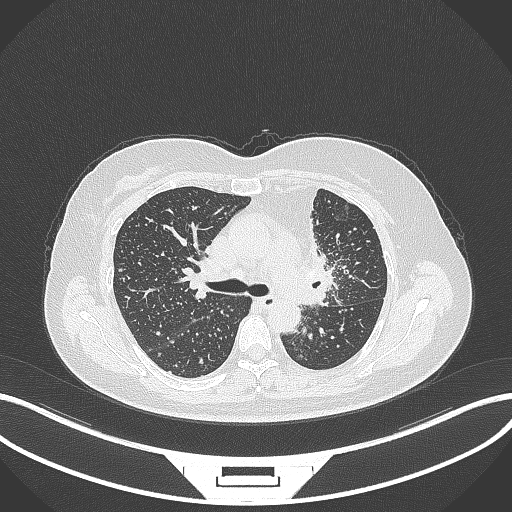
Chest CT, one axial slice. Position 213 of 348 along the scan axis. Reconstruction kernel B70f. 120 kVp. Lung window (W 1500 / L -600 HU). 1 mm slice thickness. 512 × 512 image matrix. Patient: female, 49 years. From the clinical record (not read from this slice): clinical TNM (as recorded): T1c N0 M1.
Annotated regions visible in this slice (rectangle marked by the reading radiologist):
- lung tumour (recorded histology: adenocarcinoma): bounding box [x1, y1, x2, y2] px = [294, 239, 340, 314]